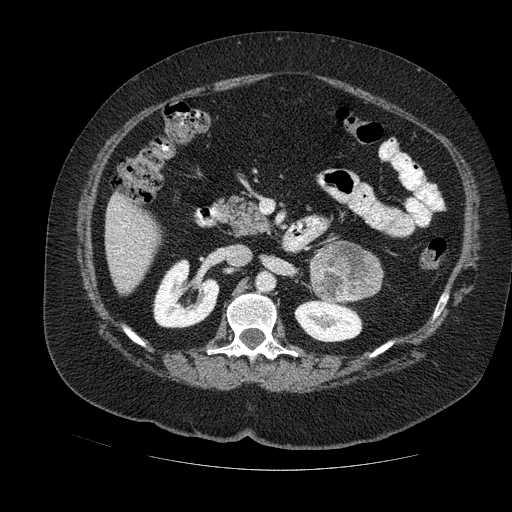
Contrast-enhanced abdominal CT, one axial slice; position 60 of 121 along the scan axis; soft-tissue window (W 400 / L 40 HU); 2.5 mm slice thickness; 512 × 512 image matrix, field of view 420 × 420 mm. Female patient. From the clinical record (not read from this slice): diagnosis: adrenocortical carcinoma; tumour side: left adrenal; tumour size at pathology: 8 cm; Ki-67 index: 7 %; stage (as recorded): 2.
Outlined on this slice (semi-automatically segmented with operator editing):
- mass: bounding box (x1, y1, x2, y2) in pixels: (311, 244, 381, 301)